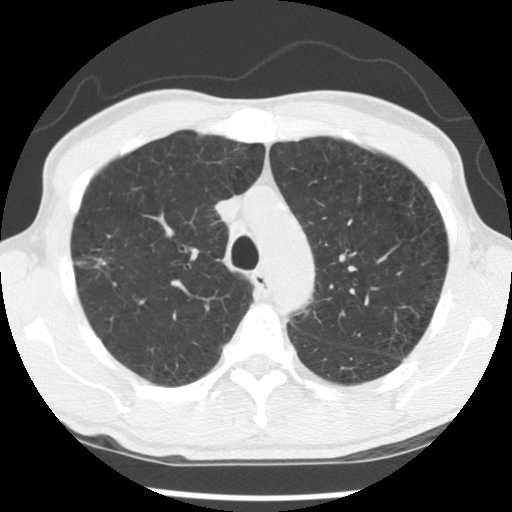
Low-dose screening chest CT, one axial slice; position 96 of 138 along the scan axis; reconstruction kernel STANDARD; 140 kVp; lung window (W 1500 / L -600 HU); 512 × 512 image matrix, field of view 320 × 320 mm.
Outlined on this slice (manually delineated by an expert):
- lesion 1 (tumor, upper lobe of right lung): bounding box [x1, y1, x2, y2] px = [97, 259, 106, 265]